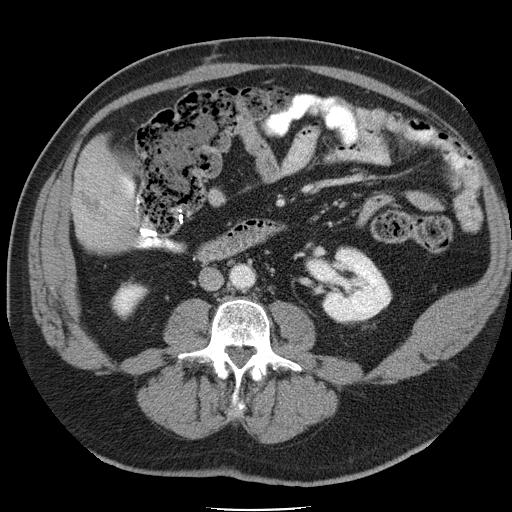
Contrast-enhanced abdominal CT, one axial slice; position 10 of 45 along the scan axis; 120 kVp; soft-tissue window (W 400 / L 40 HU); 5 mm slice thickness; 512 × 512 image matrix. Male patient, age 65 years. From the clinical record (not read from this slice): diagnosis: colorectal cancer liver metastases, imaged before liver resection; multiple liver metastases: yes; largest metastasis: 4.9 cm; disease in both lobes: no.
Outlined on this slice (manually delineated by an expert):
- liver: bounding box <73,144,131,253> (left, top, right, bottom; pixels)
- liver metastasis: <80,174,112,220>